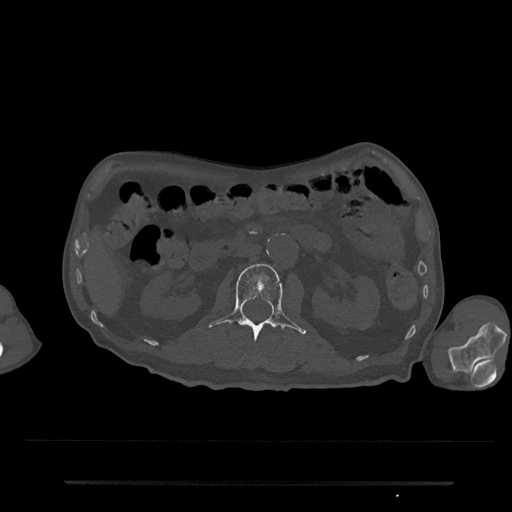
CT including the spine, one axial slice. Slice 68 of 797 in the series (ordered by position). 120 kVp. Bone window (W 1800 / L 400 HU). 0.5 mm slice thickness. 512 × 512 image matrix, field of view 427 × 427 mm. Patient: male, 74 years. From the clinical record (not read from this slice): primary cancer: prostate.
Outlined on this slice (semi-automatic segmentation, software-assisted and operator-edited):
- L2 vertebra: bounding box [x1, y1, x2, y2] px = [208, 263, 306, 340]